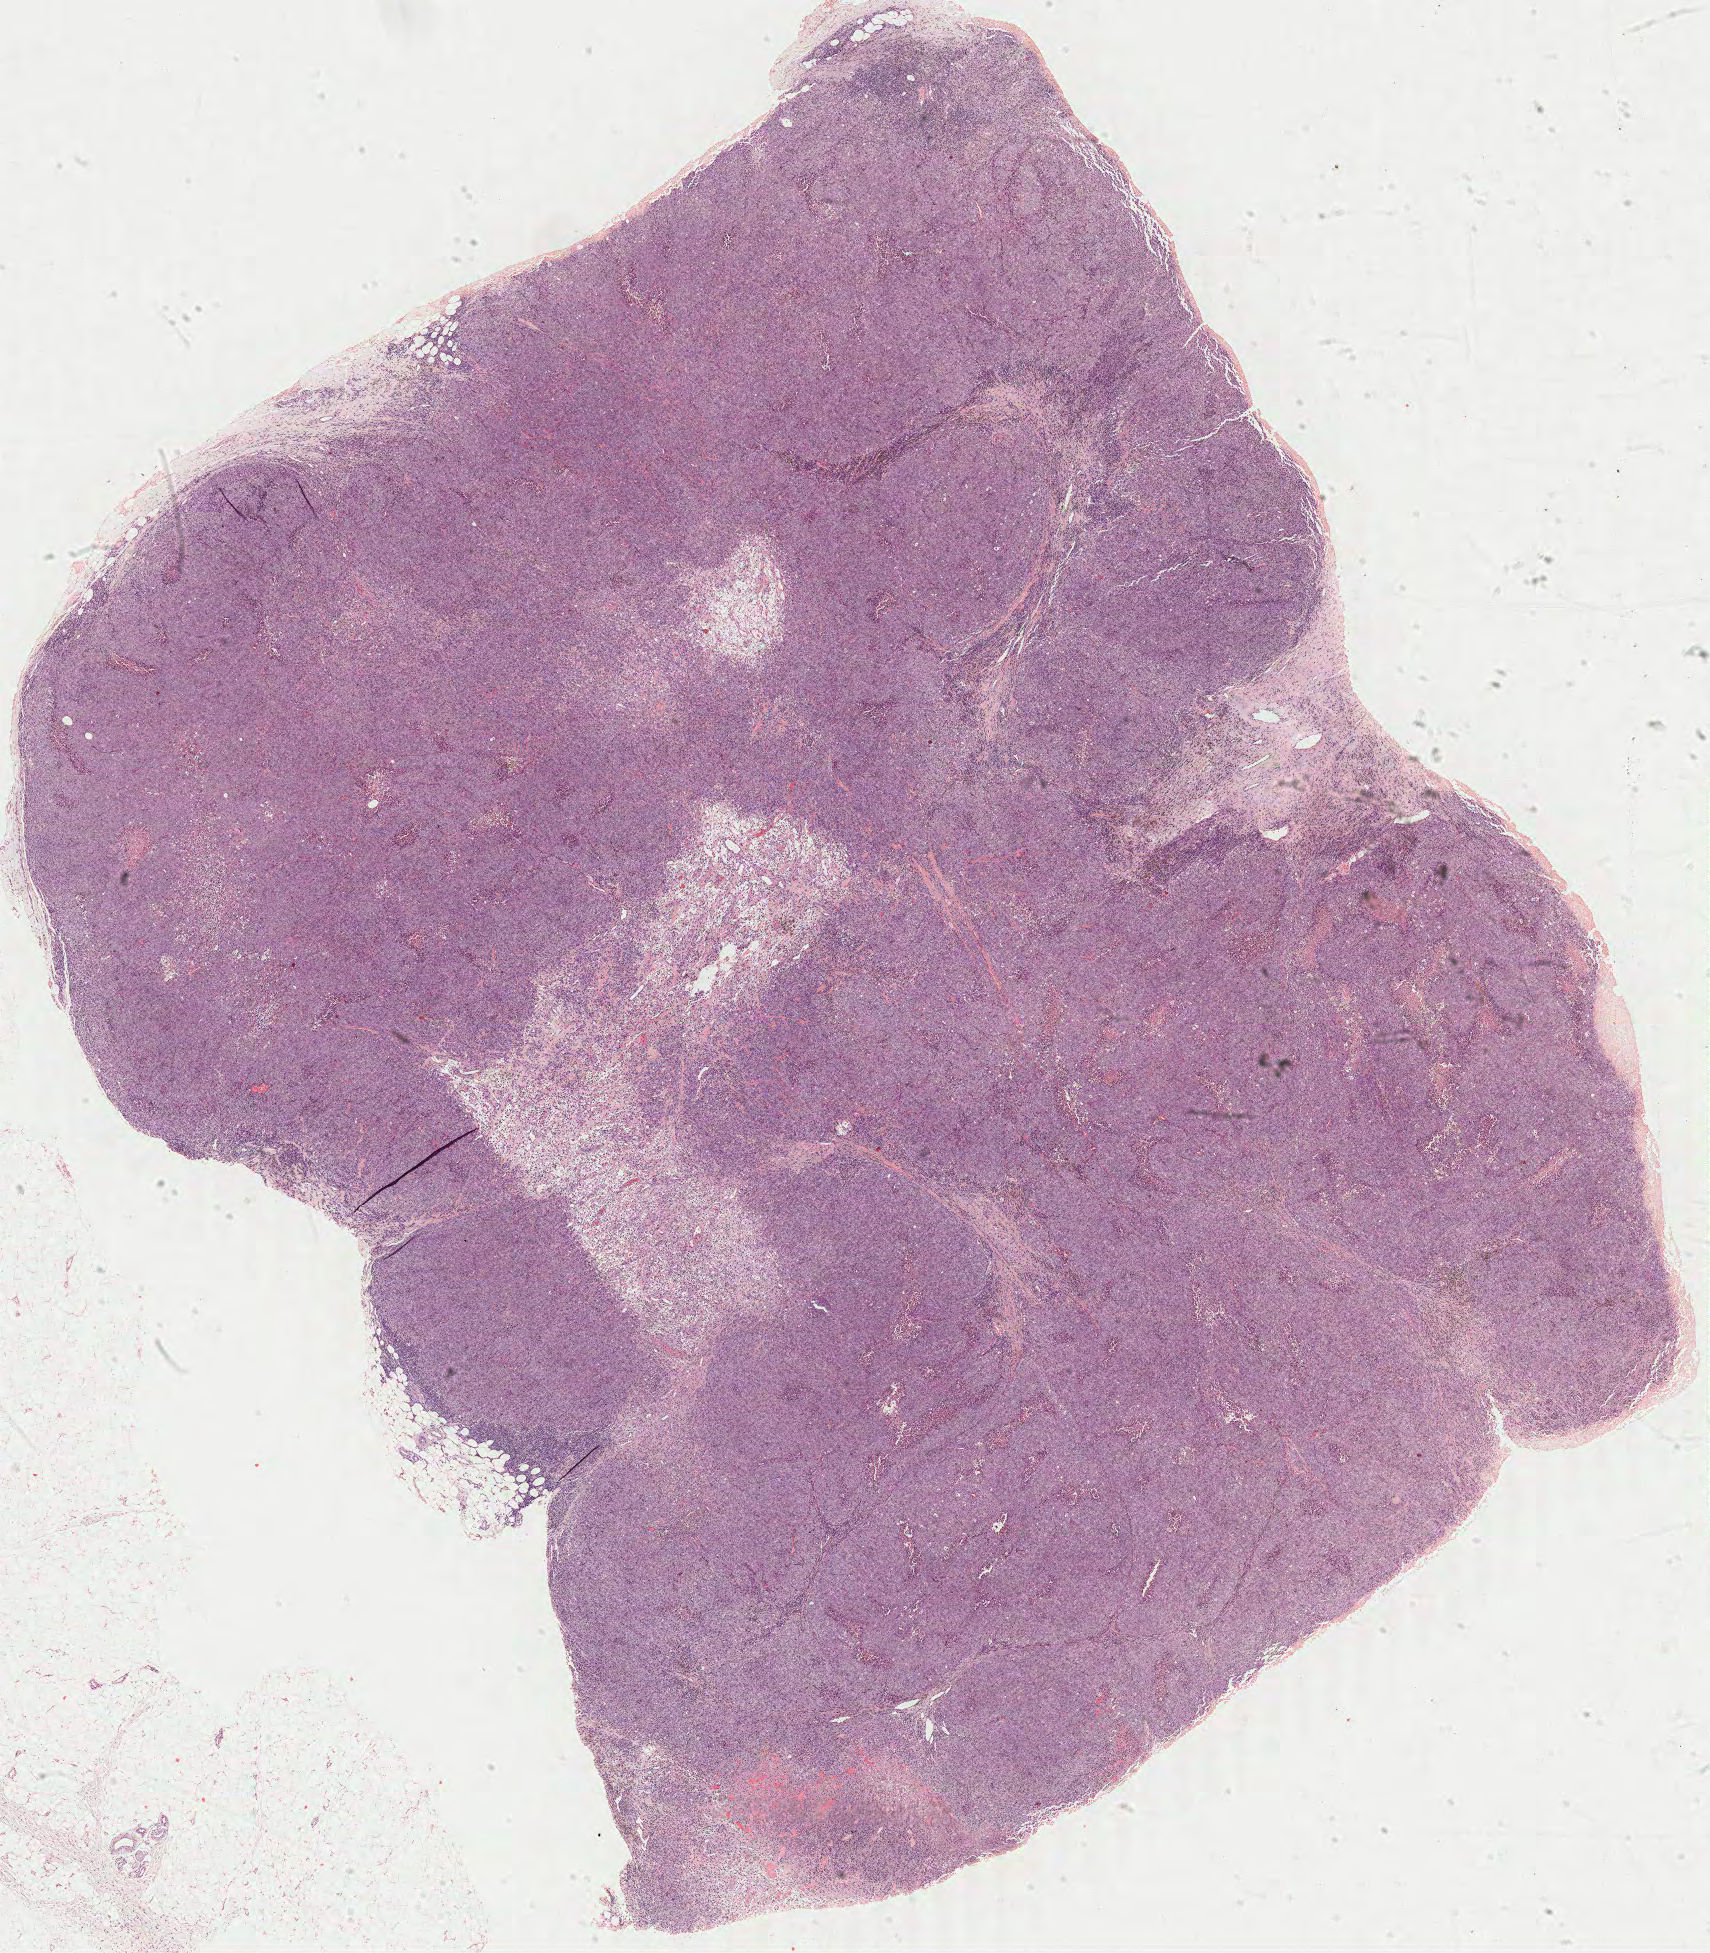
Whole-slide histology image, Hematoxylin and eosin (H&E) stained — shown as a low-resolution overview of the whole scanned area (about 13.7 x 15.7 mm), FFPE section, metastatic tumour sample, sampled site: connective, subcutaneous and other soft tissues of pelvis. Male, age 45 years at initial diagnosis.
This section: metastatic tumour tissue. Patient diagnosis: Malignant melanoma, NOS.